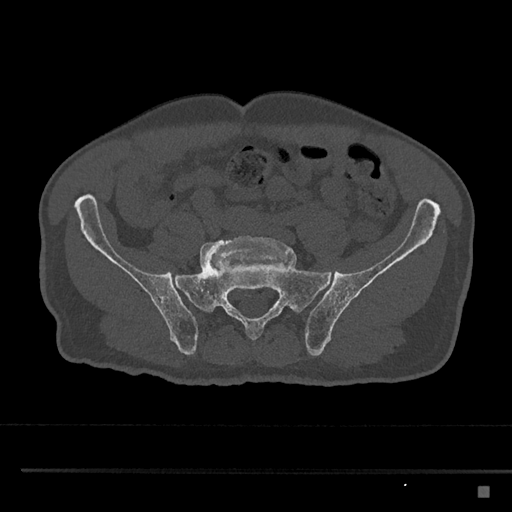
CT including the spine, one axial slice; slice 542 of 797 in the series (ordered by position); reconstruction kernel Br40s/3; 120 kVp; bone window (W 1800 / L 400 HU); 0.5 mm slice thickness; 512 × 512 image matrix. Male patient, age 59 years. Case-level facts recorded for this patient, not image findings: primary cancer: prostate.
Annotated regions visible in this slice (semi-automatic segmentation, software-assisted and operator-edited):
- L5 vertebra: box from (x=200, y=235) to (x=292, y=272) px